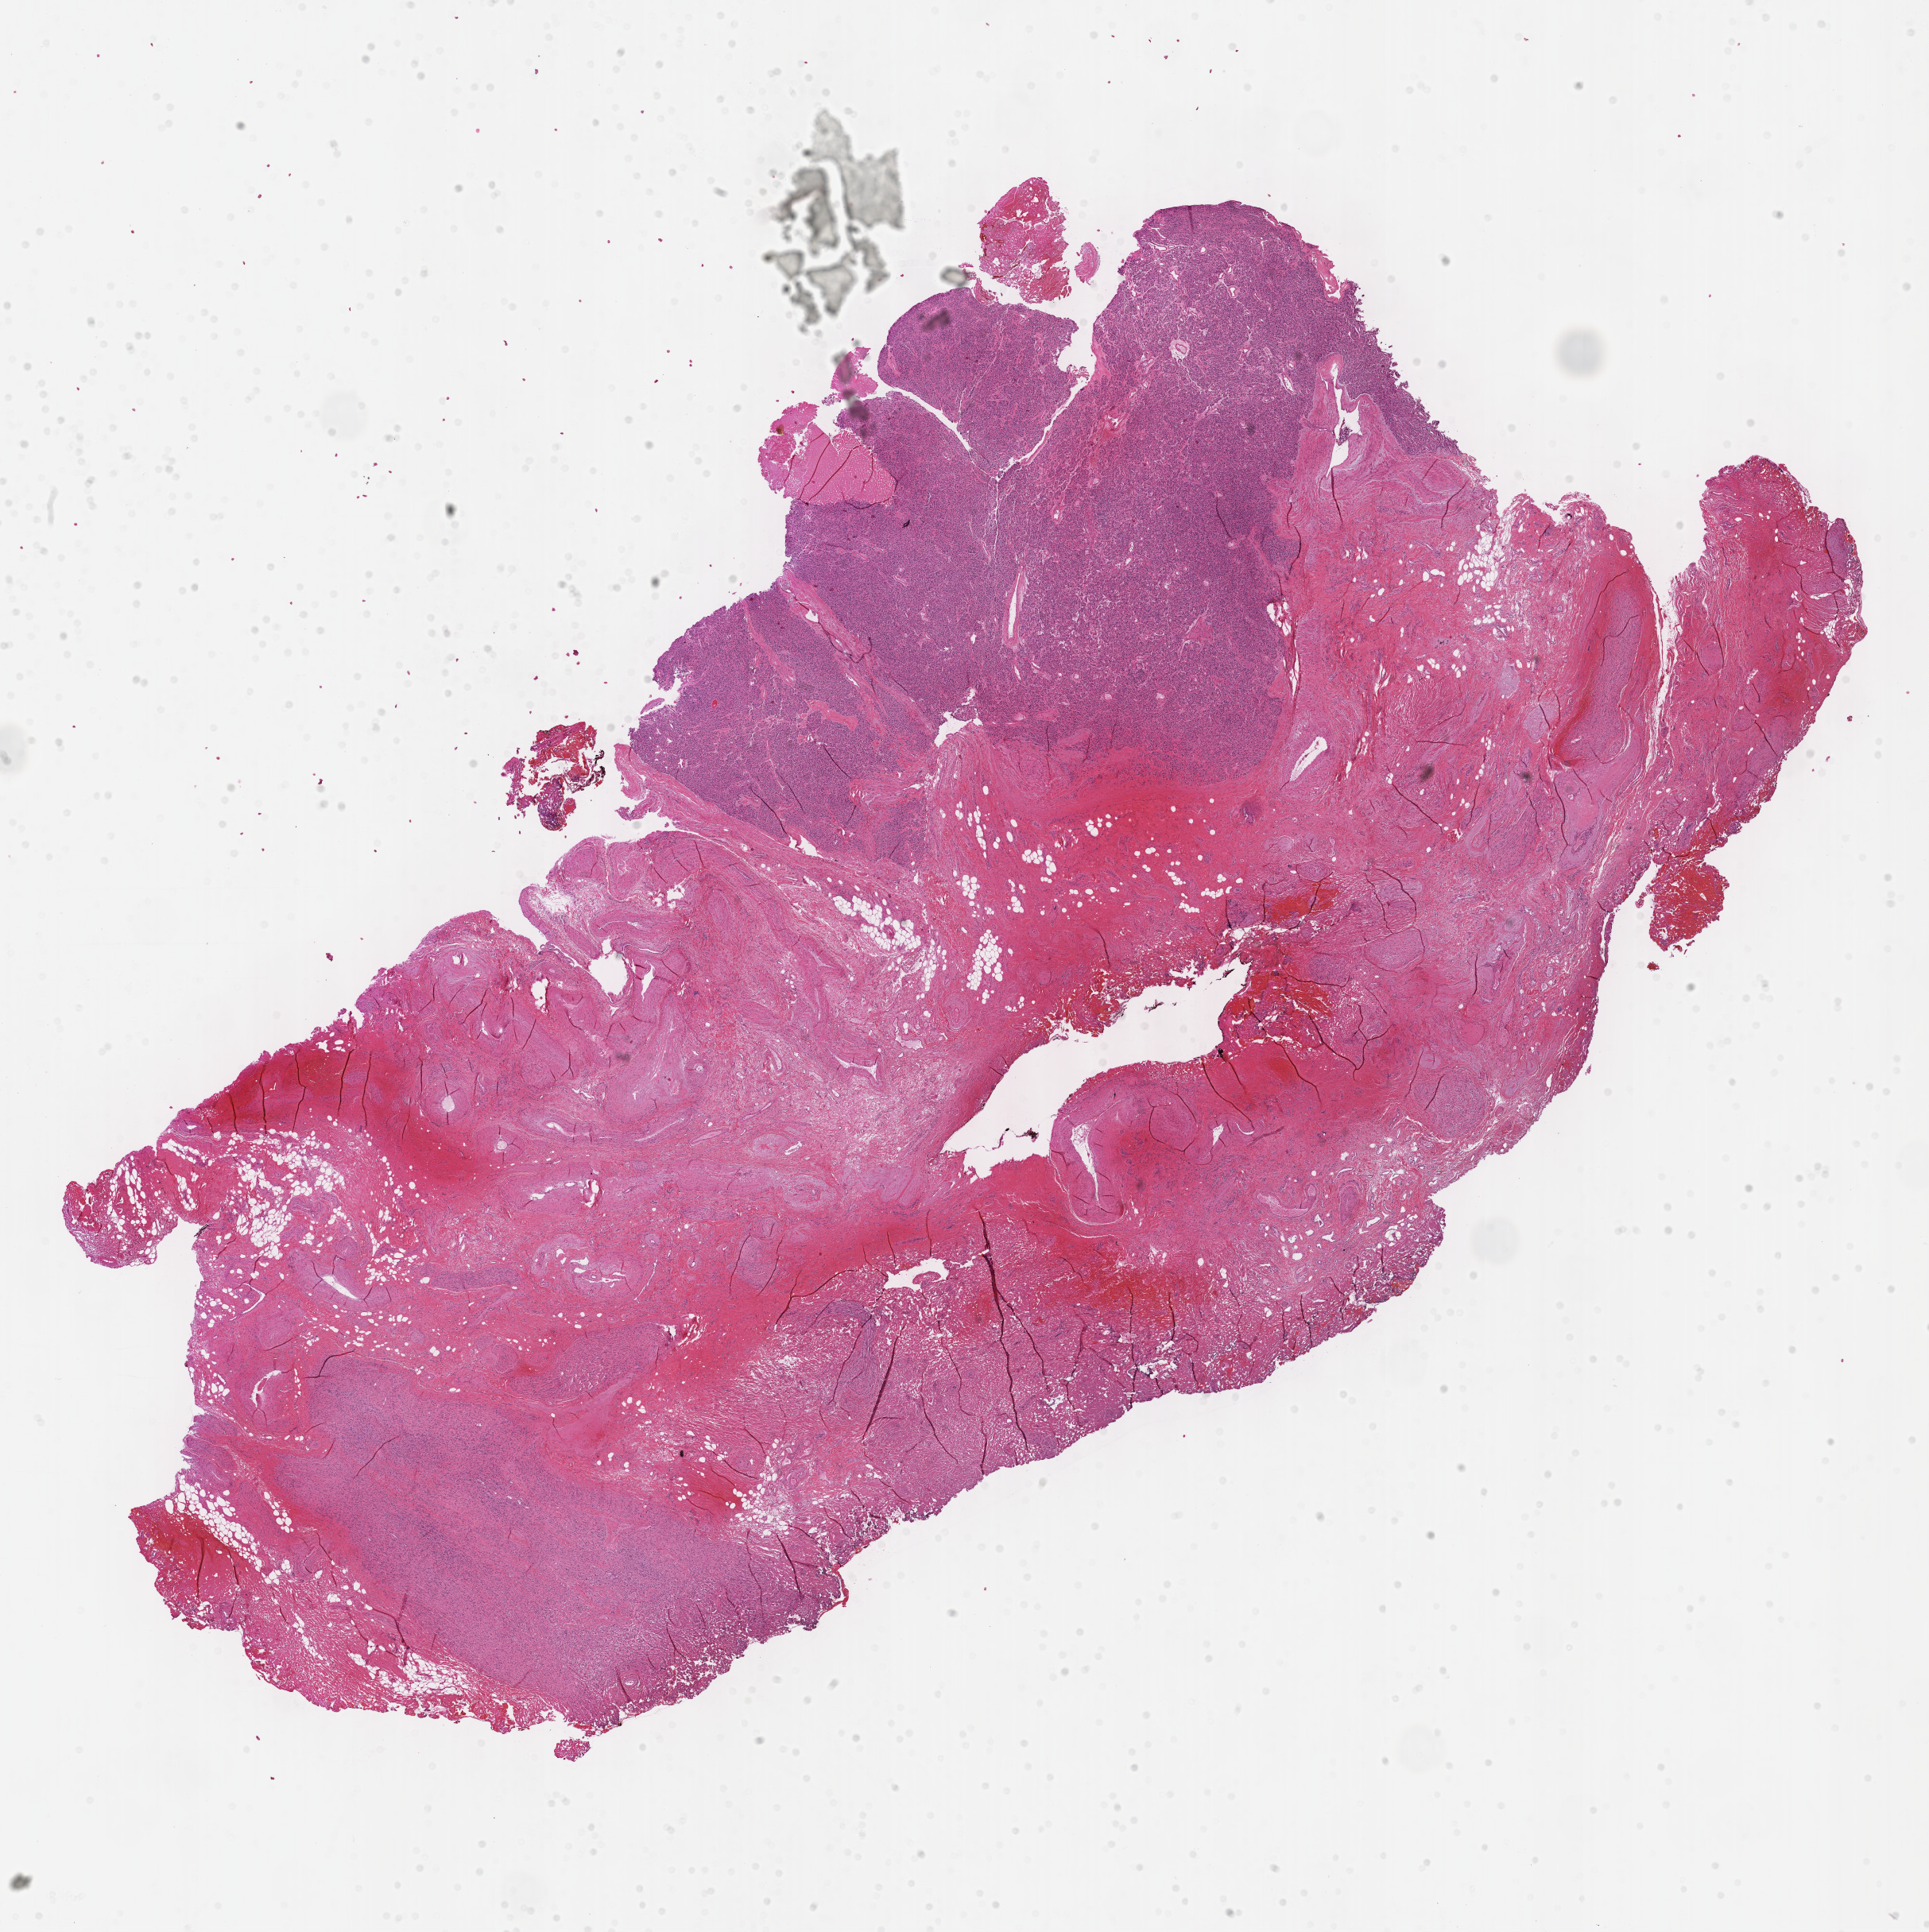
Digitized Hematoxylin and eosin (H&E) stained tissue section (whole slide), a low-resolution overview of the entire scanned area, about 19.6 x 19.7 mm. Formalin-fixed paraffin-embedded (FFPE) diagnostic section. Sample: primary tumour, connective, subcutaneous and other soft tissues. Male patient; age at initial diagnosis 53 years.
• diagnosis: Paraganglioma, NOS (connective, subcutaneous and other soft tissues of thorax)